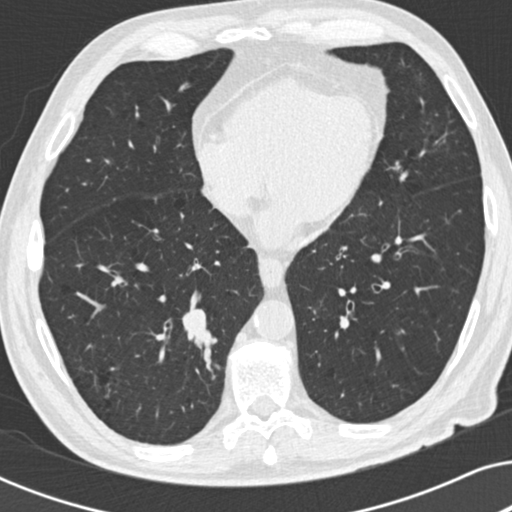
Low-dose screening chest CT, one axial slice; slice 85 of 191 in the series (ordered by position); lung window (W 1500 / L -600 HU); 2 mm slice thickness; 512 × 512 image matrix.
Structures marked on this image (expert manual segmentation):
- lesion 1 (tumor, lower lobe of right lung): bounding box [x1, y1, x2, y2] px = [181, 309, 205, 339]